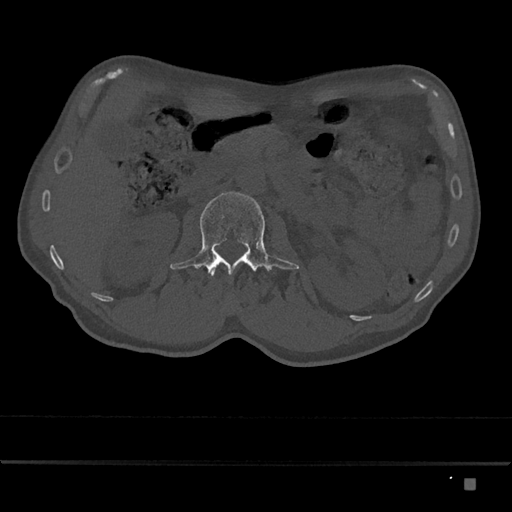
CT including the spine, one axial slice. Position 485 of 797 along the scan axis. Bone window (W 1800 / L 400 HU). 0.5 mm slice thickness. 512 × 512 image matrix, field of view 390 × 390 mm. Male patient, age 72 years. From the clinical record (not read from this slice): primary cancer: prostate.
Annotated regions visible in this slice (semi-automatically segmented with operator editing):
- L1 vertebra: box from (x=210, y=270) to (x=215, y=277) px
- L2 vertebra: (x=170, y=191)–(x=299, y=275)